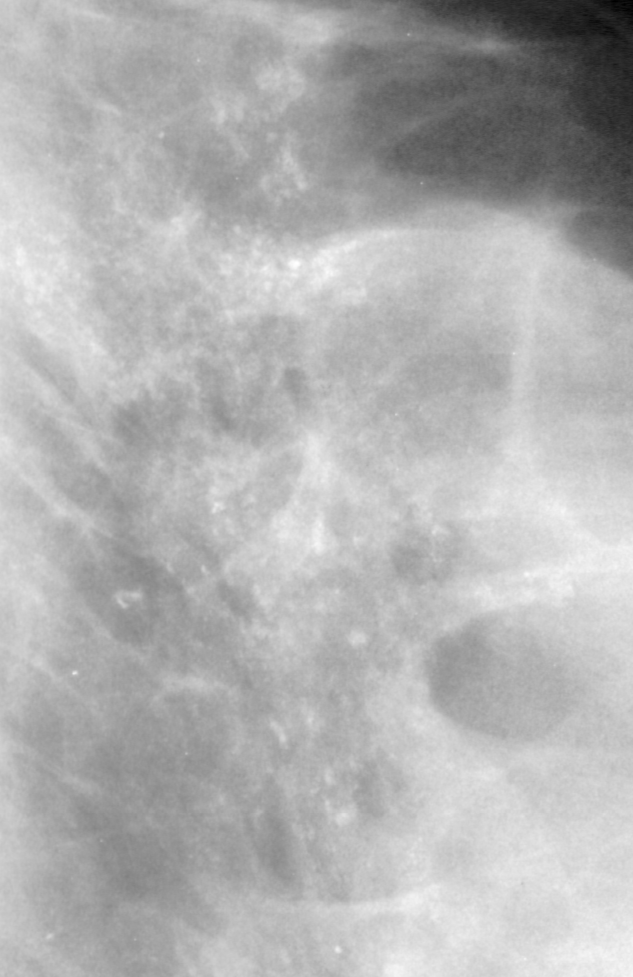
Crop from a digitized film mammogram around one marked abnormality, right breast, CC view.
- Calcifications, morphology pleomorphic, distribution segmental; BI-RADS assessment category 4; subtlety rating 3 on a 1 (subtle) to 5 (obvious) scale; pathology (as recorded): benign.